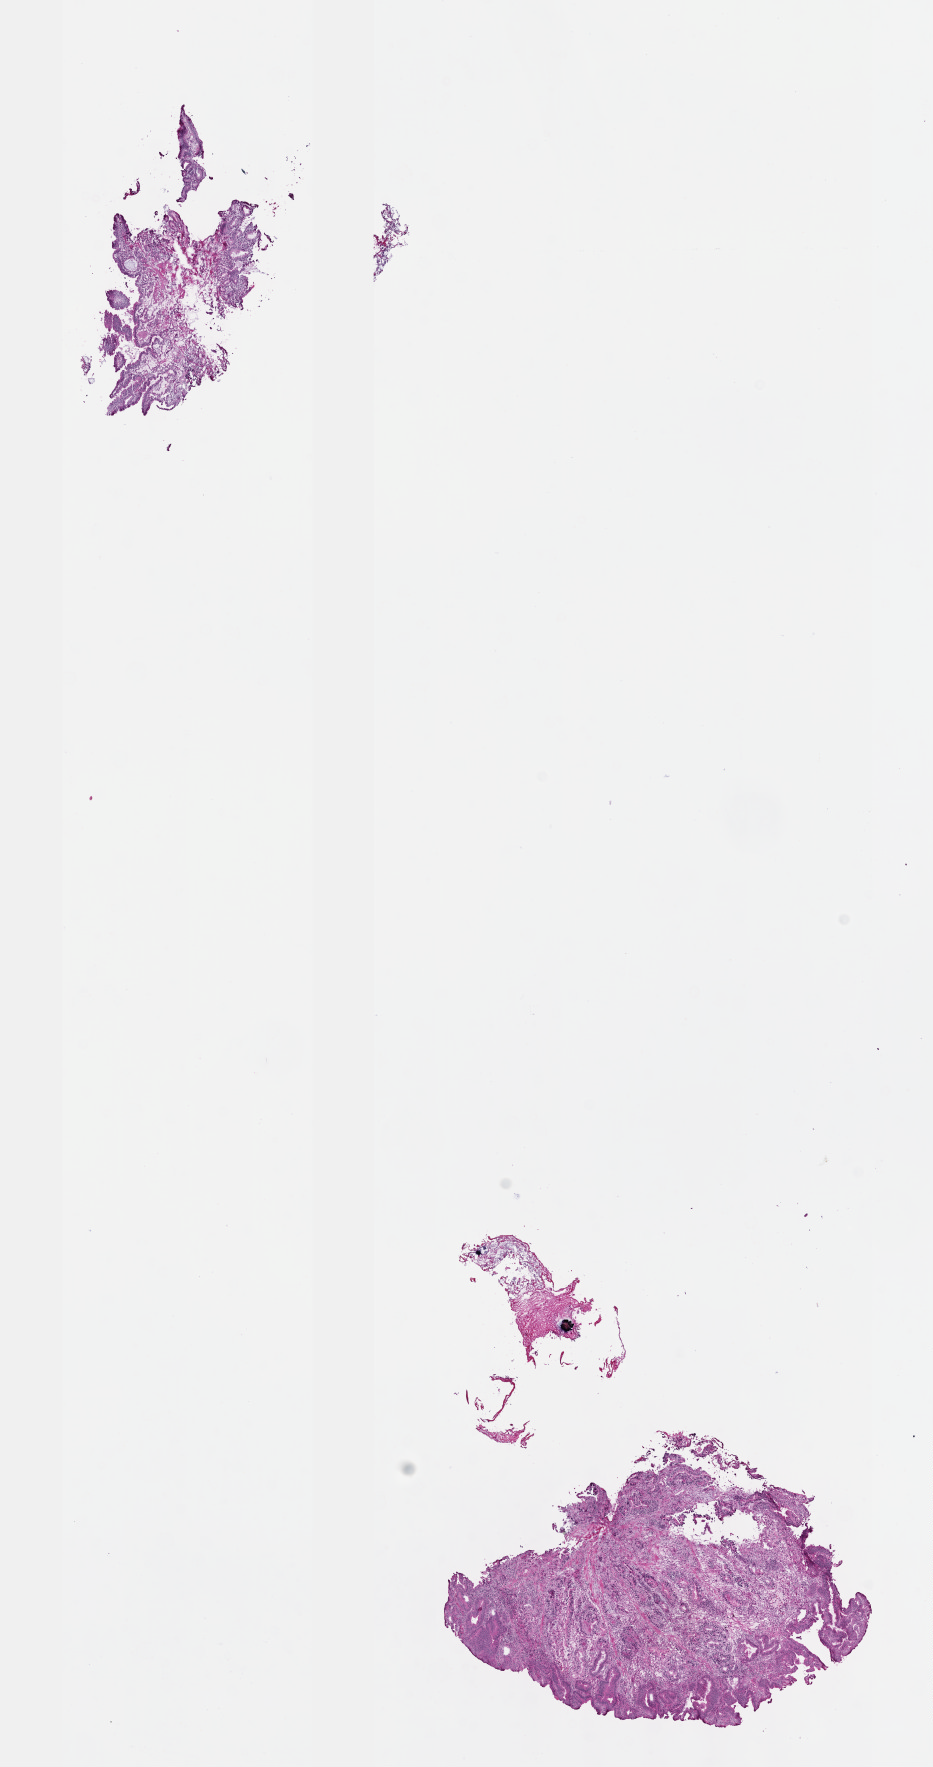
Whole-slide histology image, Hematoxylin and eosin (H&E) stained, shown as a low-resolution overview of the whole scanned area (about 7.5 x 14.3 mm, slide scanned at 40x). Frozen section. Esophagus, primary tumour sample. Patient: male, age at initial diagnosis 74 years. Histologic grade: G2 (moderately differentiated). Pathologist review of this section (percent, as recorded): tumour cells 85%, tumour nuclei 60%, normal cells 15%, stromal cells 0%, necrosis 0%. Infiltration values recorded for this section: lymphocyte infiltration 5%, monocyte infiltration 0%, neutrophil infiltration 1%.
Pathologic diagnosis: Adenocarcinoma, NOS (lower third of esophagus).